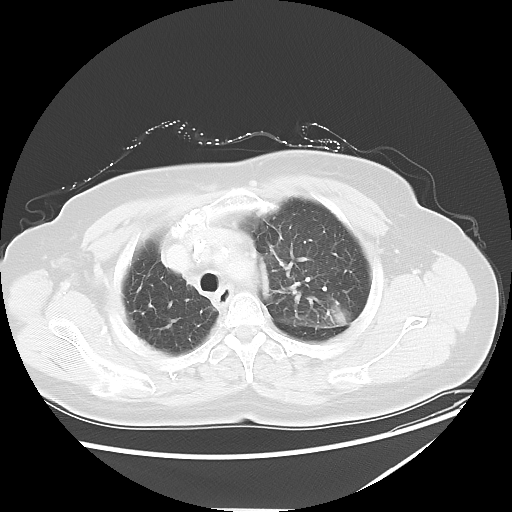
Chest CT, one axial slice. Position 43 of 54 along the scan axis. Reconstruction kernel LUNG. 120 kVp. Lung window (W 1500 / L -600 HU). 512 × 512 image matrix, field of view 384 × 384 mm. Female patient, age 61 years. From the clinical record (not read from this slice): clinical TNM (as recorded): T1c N3 M1.
Outlined on this slice (rectangle marked by the reading radiologist):
- lung tumour (recorded histology: adenocarcinoma): bounding box [x1, y1, x2, y2] px = [315, 296, 358, 330]